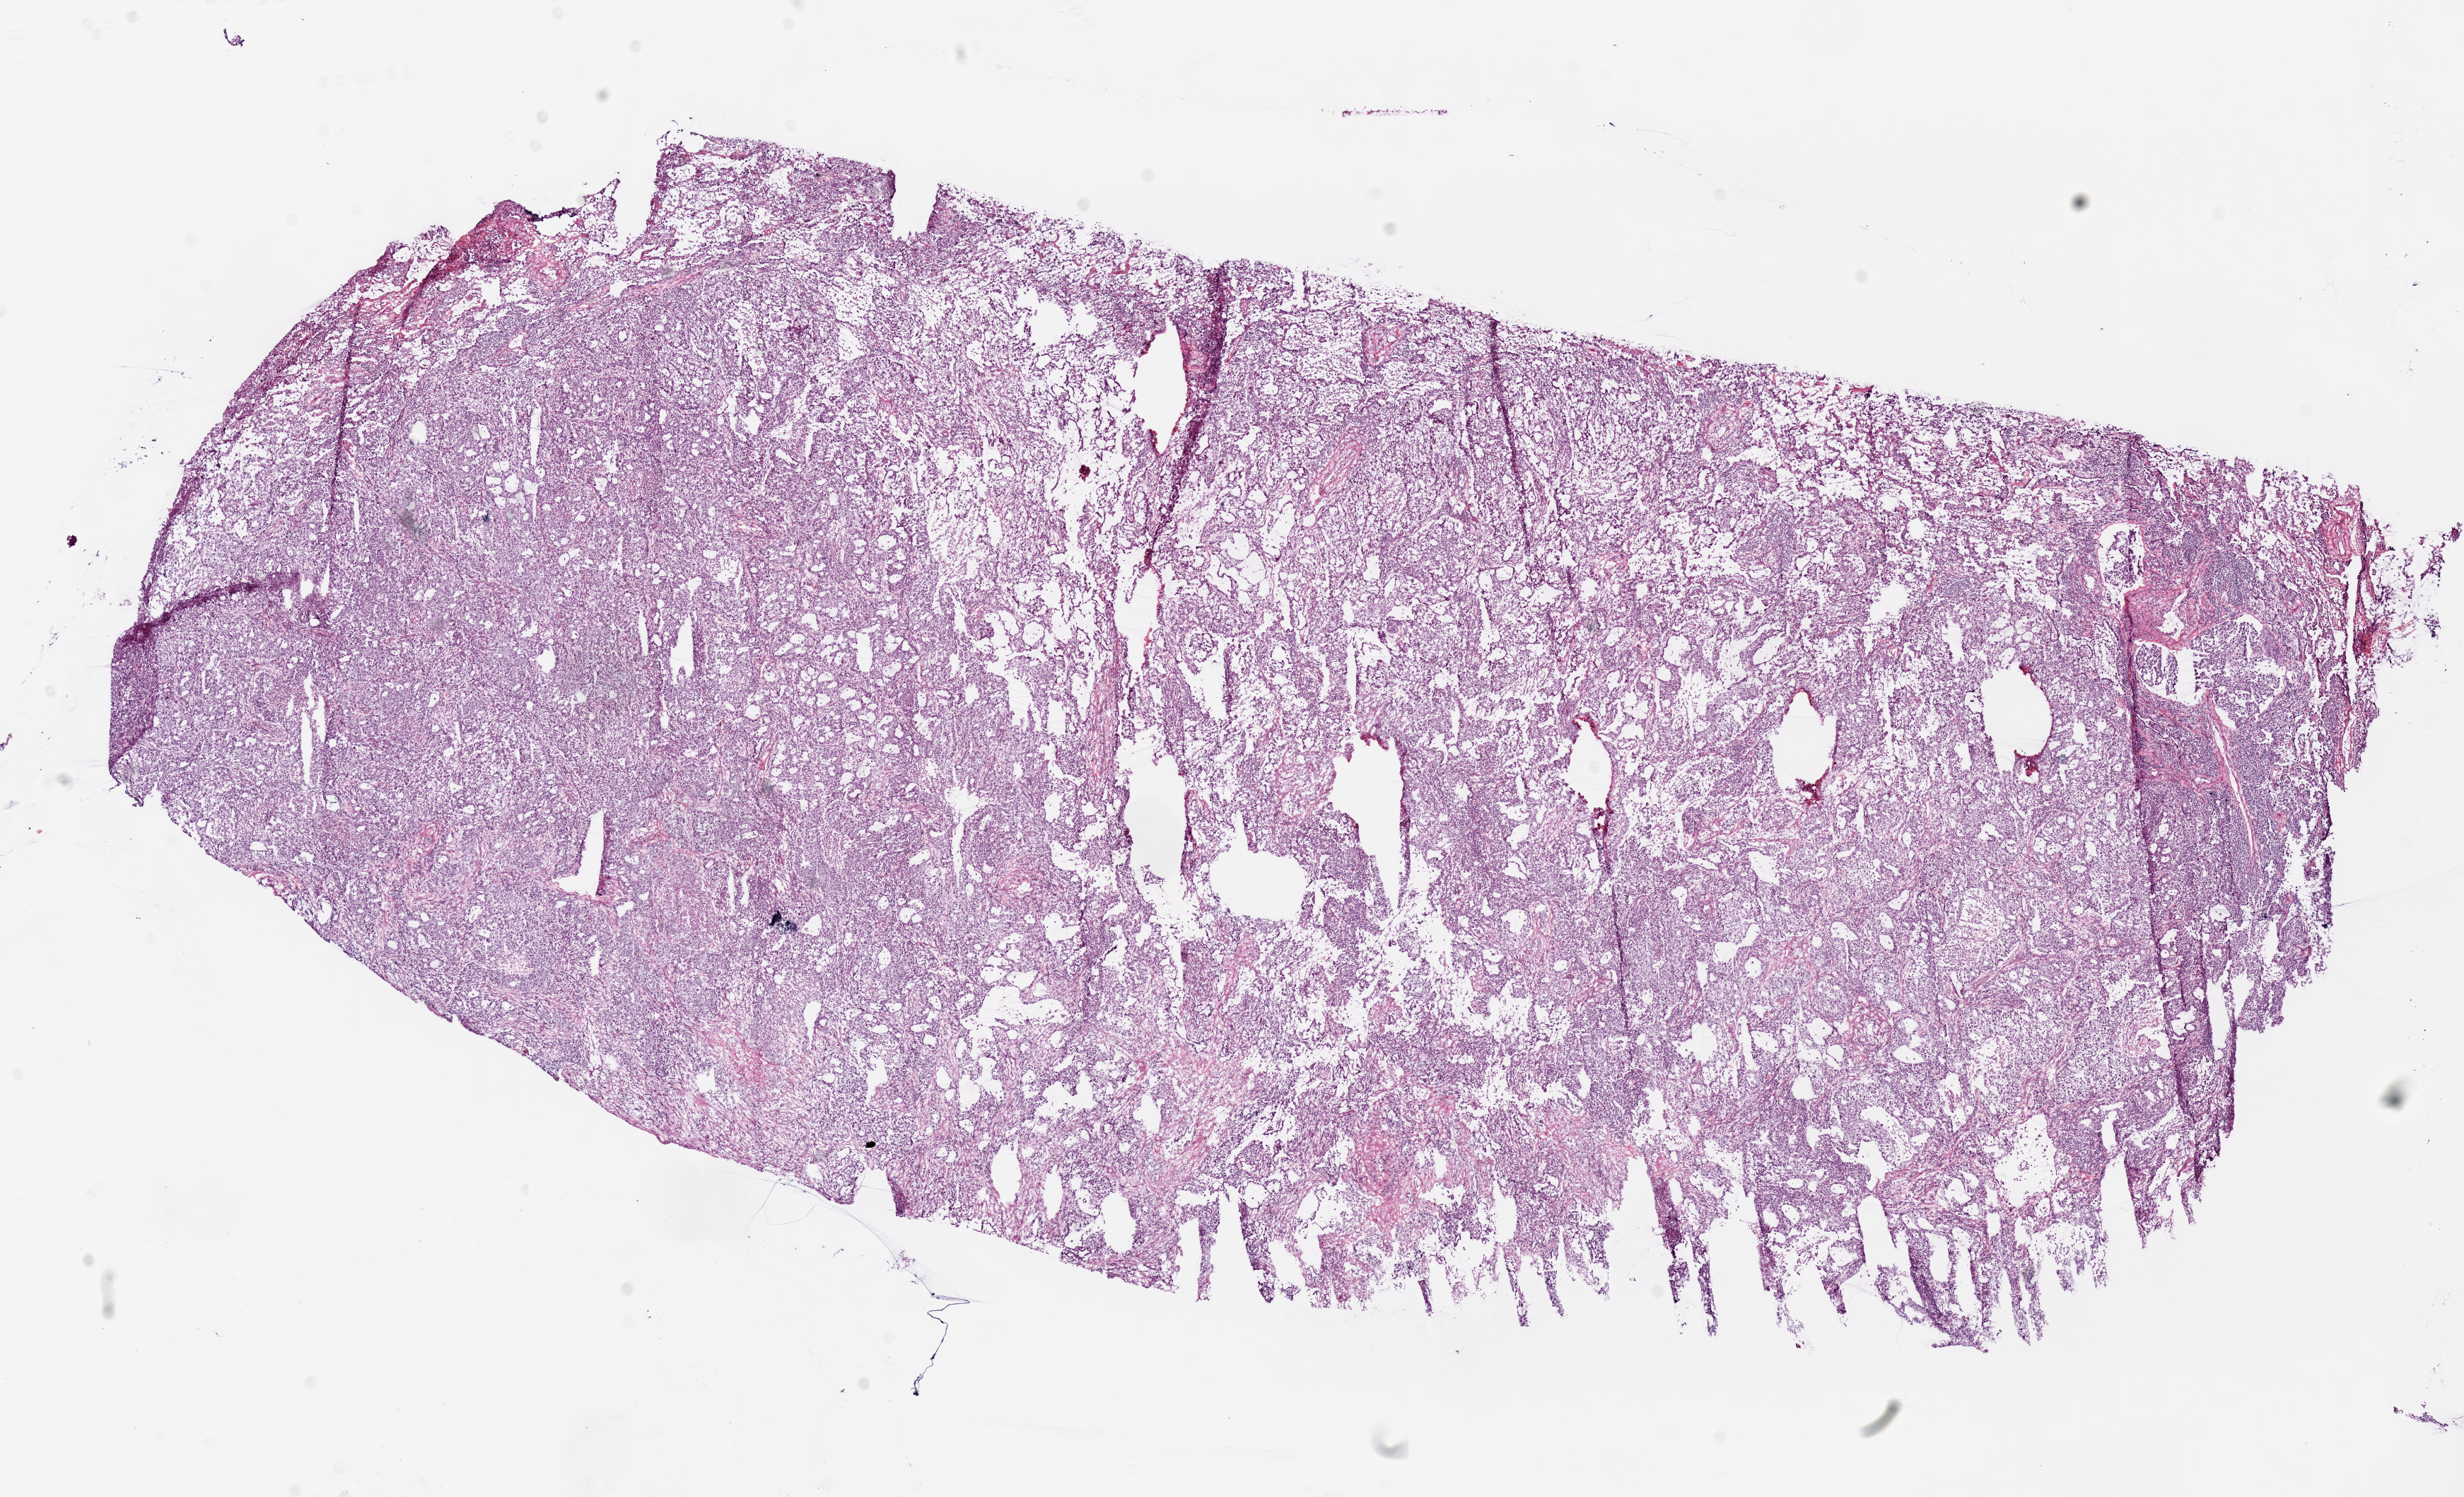
Digitized H&E-stained tissue section (whole slide) — whole scanned area (about 13.8 x 8.4 mm) shown as a low-resolution overview. Frozen section. Sample: primary tumour, lung. Female, age 59 years at initial diagnosis. Pathologist review of this section (percent, as recorded): tumour cells 83%, tumour nuclei 70%, normal cells 5%, stromal cells 10%, necrosis 2%.
* AJCC pathologic stage: IB (7th edition)
* TNM: T2 N0 MX
* histologic diagnosis: Adenocarcinoma, NOS (lower lobe, lung)